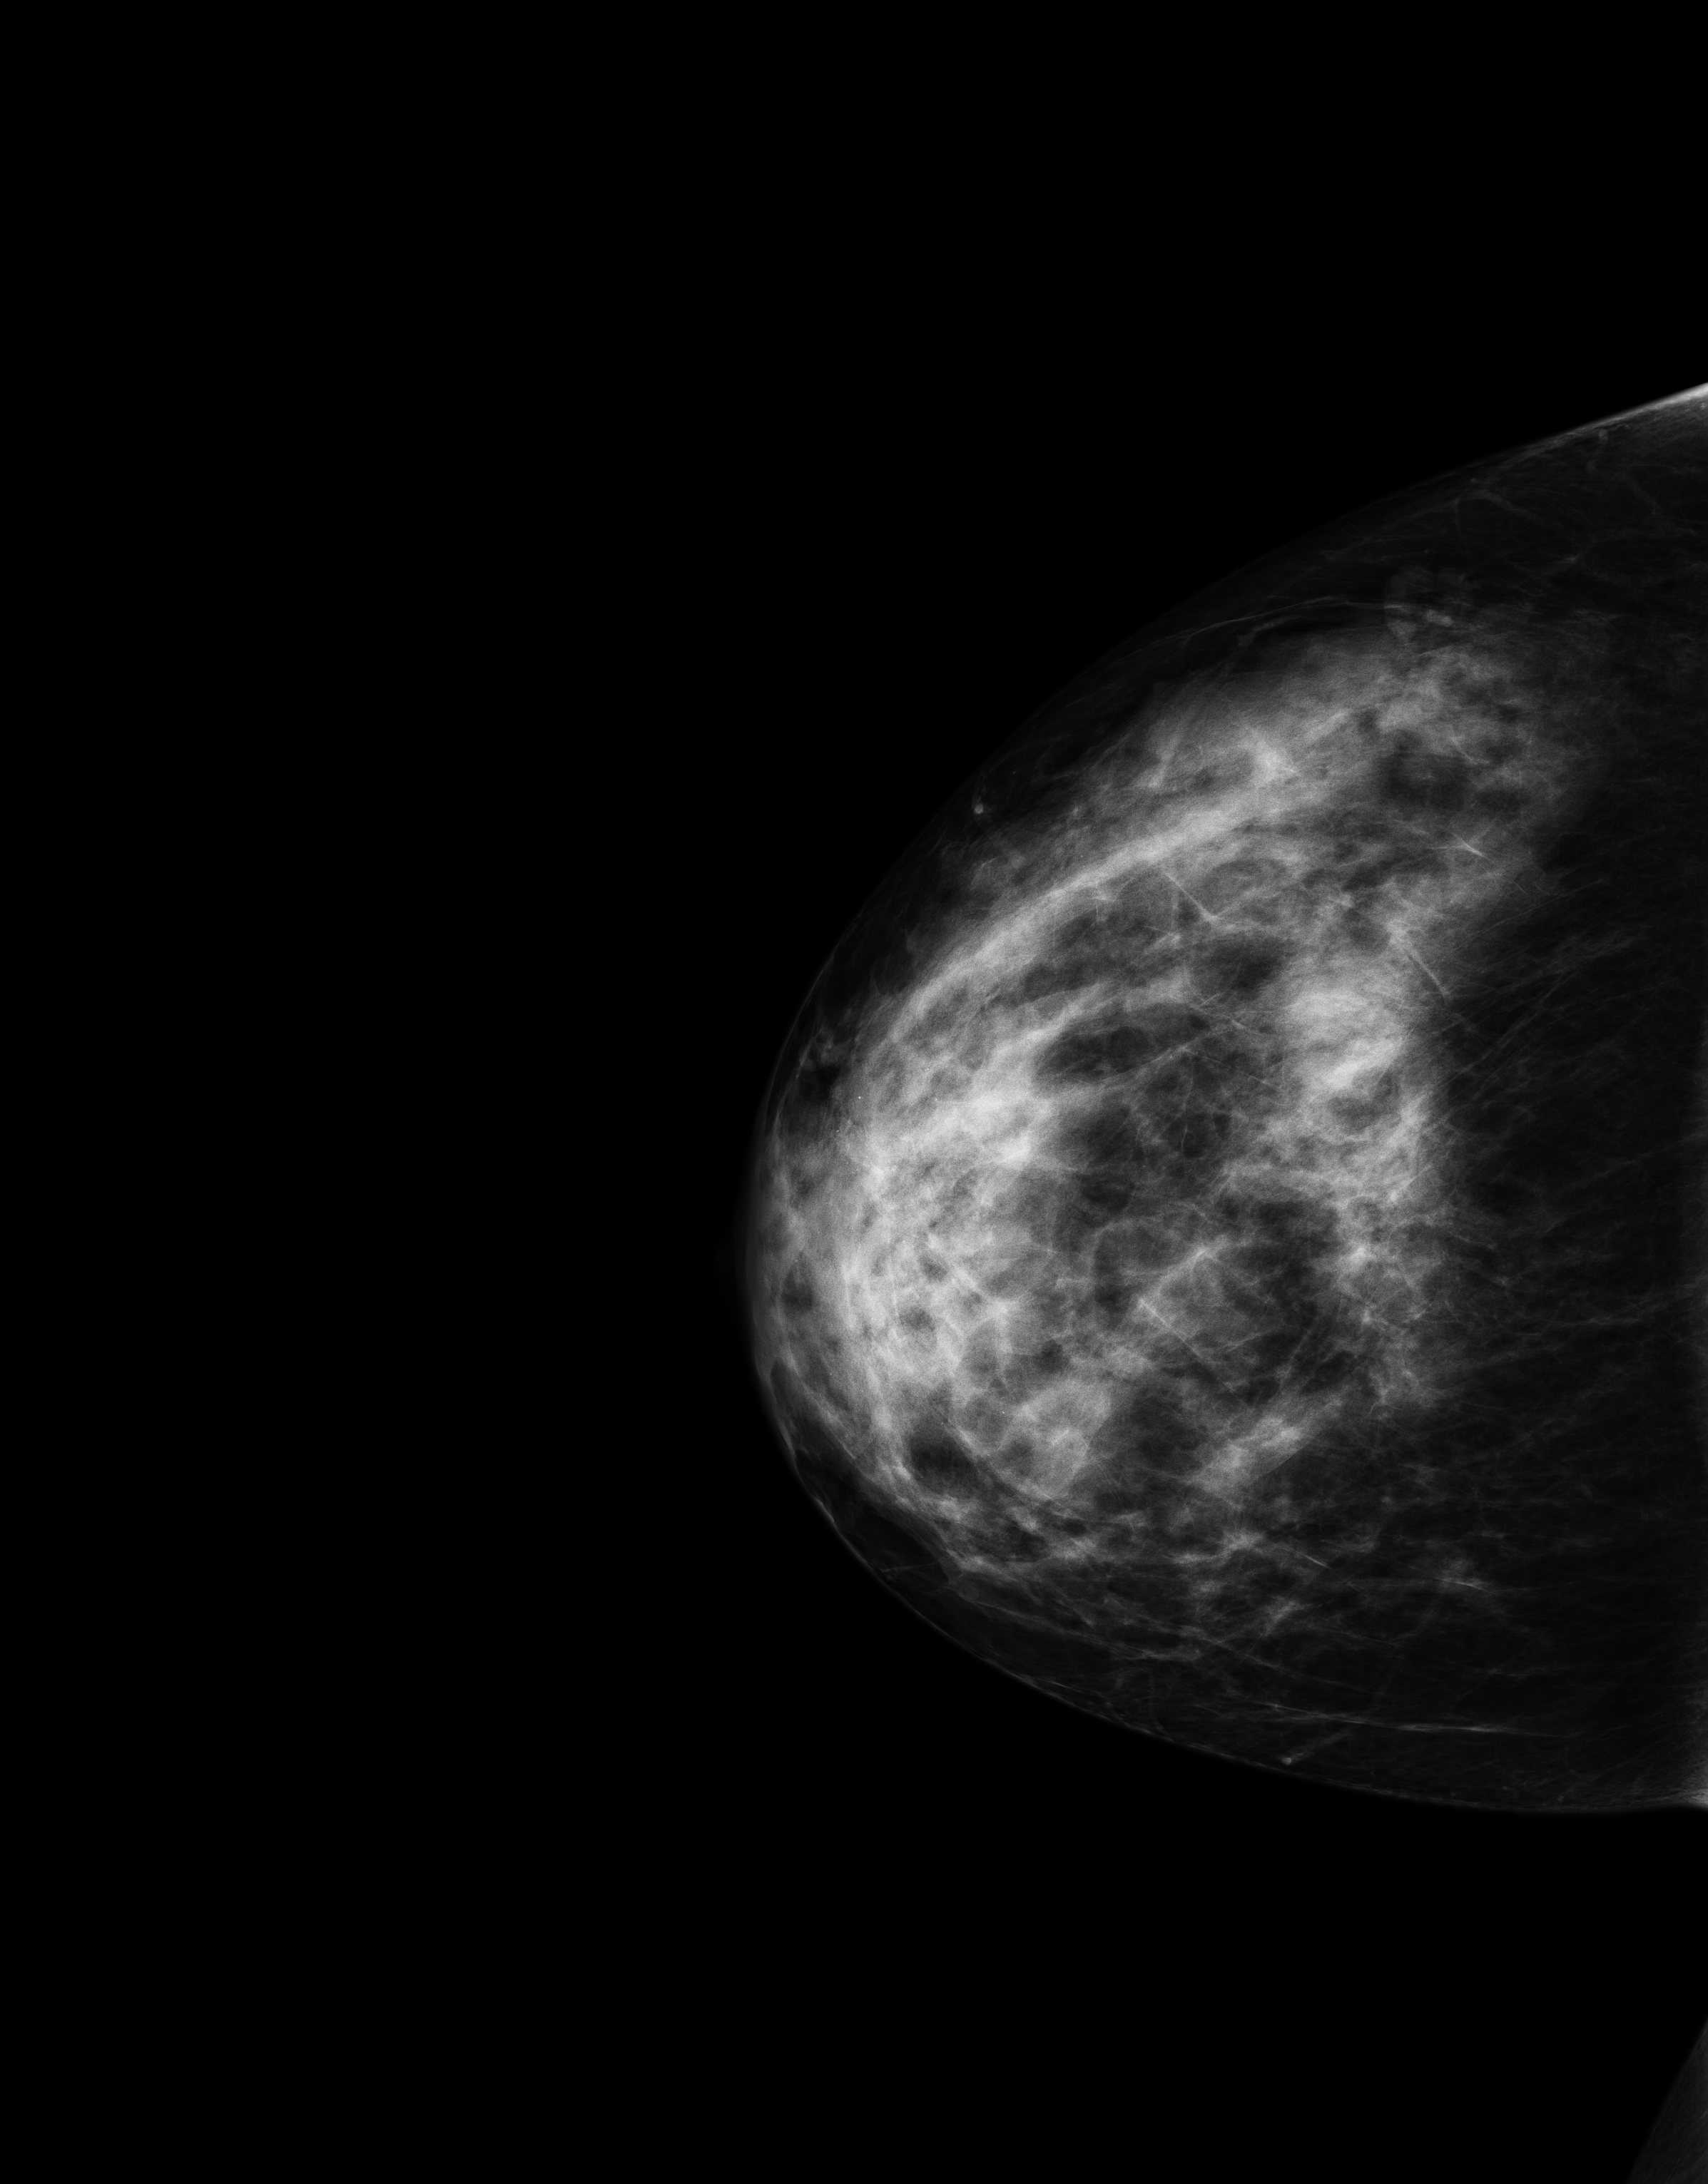
Full-field digital mammogram (FFDM); right breast; CC view; annual screening mammography examination; system: Senographe Essential ADS_56.21.3. Patient aged 46 years (female).
BI-RADS breast density category at the screening exam (both breasts, scale 1–4): 3. Final BI-RADS category for the screening round (tomosynthesis exam, both breasts): category 1. Recall: no recall after this screen.